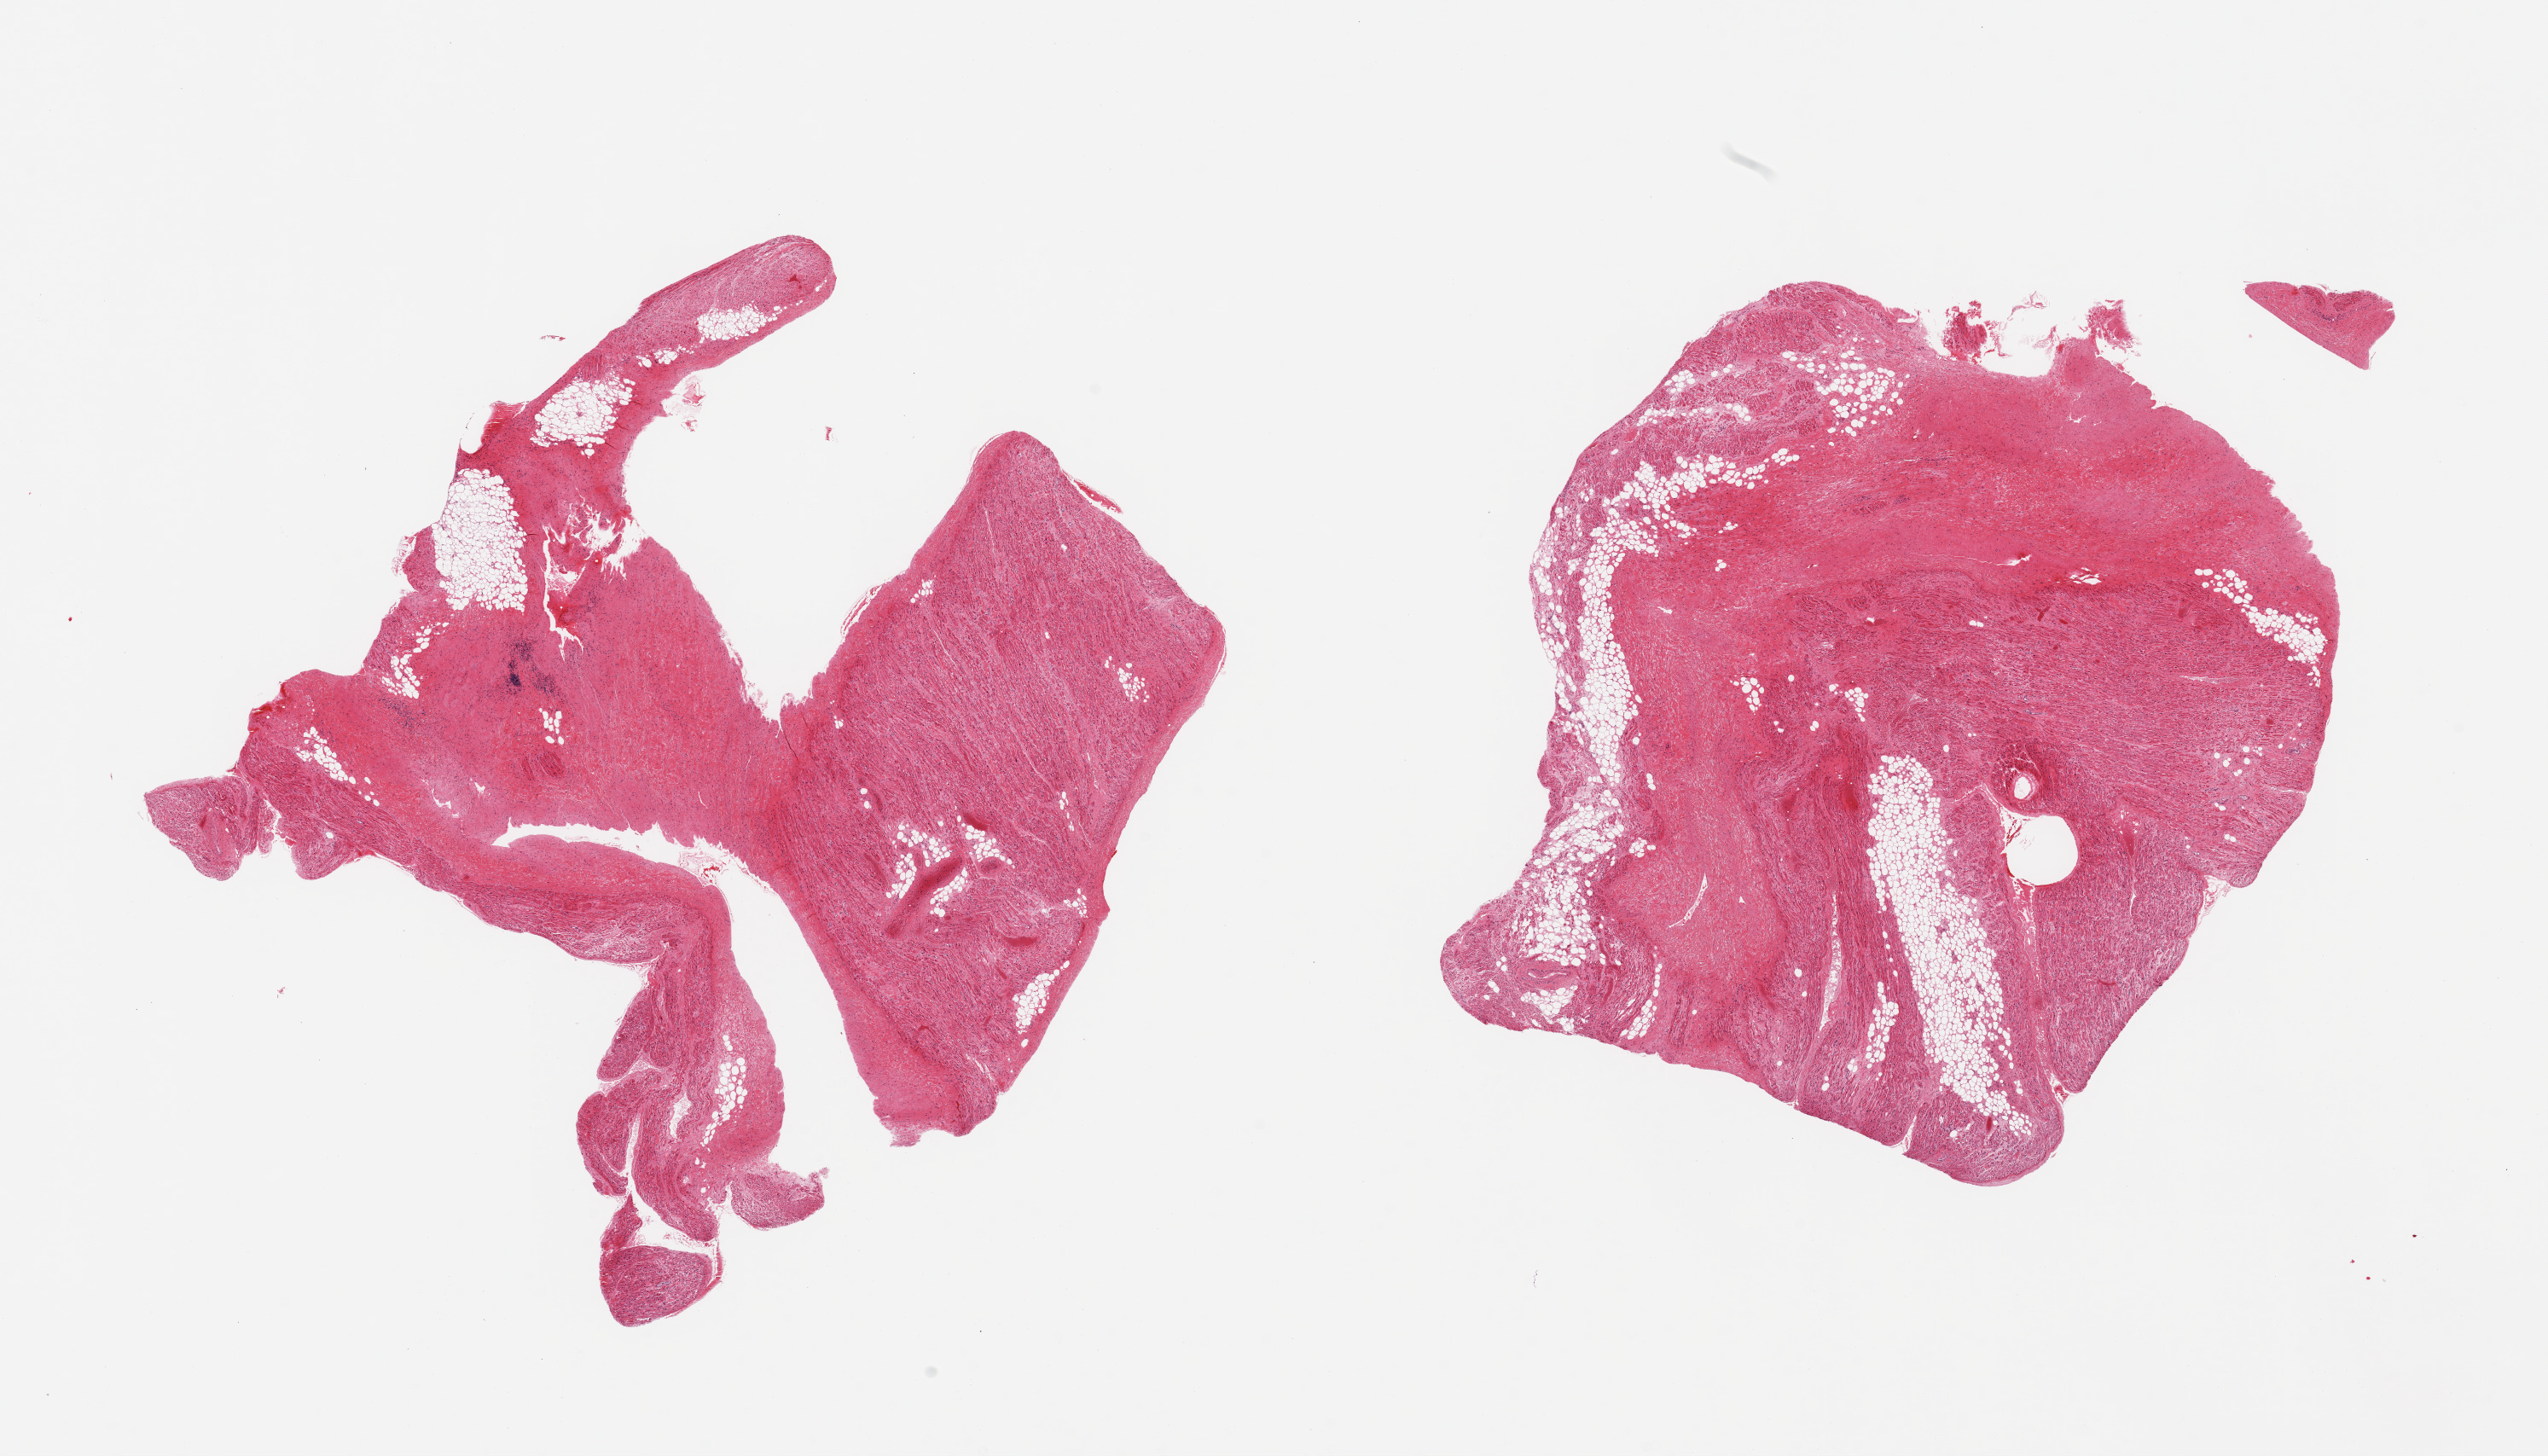
Digitized hematoxylin and eosin (H&E)-stained section, brightfield — whole scanned area (about 23.6 x 13.5 mm, acquisition: 20x scan) shown as a low-resolution overview; PAXgene-fixed paraffin-embedded (PFPE) section; section of auricular appendage (target tissue); donor tissue sample. Donor: female.
Review note (as recorded): 2 pieces; 50% internal fibrofatty content.